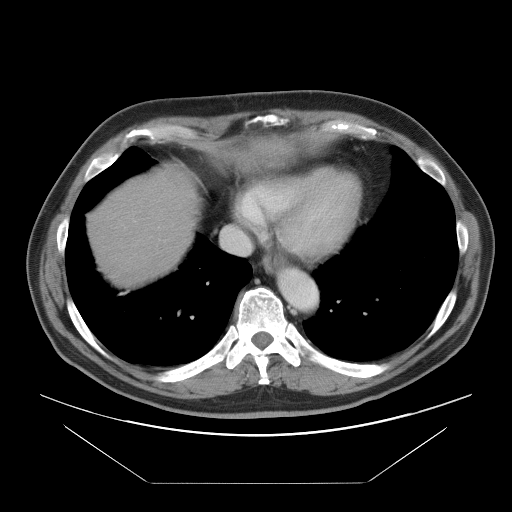
Contrast-enhanced abdominal CT, one axial slice. Position 86 of 97 along the scan axis. 120 kVp. Intravenous contrast given. Soft-tissue window (W 400 / L 40 HU). 512 × 512 image matrix, field of view 442 × 442 mm. Male patient, age 62 years. From the clinical record (not read from this slice): diagnosis: colorectal cancer liver metastases, imaged before liver resection; multiple liver metastases: no; largest metastasis: 7 cm; disease in both lobes: yes.
Annotated regions visible in this slice (outlined manually by an expert reader):
- hepatic veins: box from (x=221, y=194) to (x=264, y=256) px
- liver: (x=91, y=144)–(x=256, y=283)
- planned liver remnant (the part of the liver to remain after resection): (x=91, y=185)–(x=195, y=284)